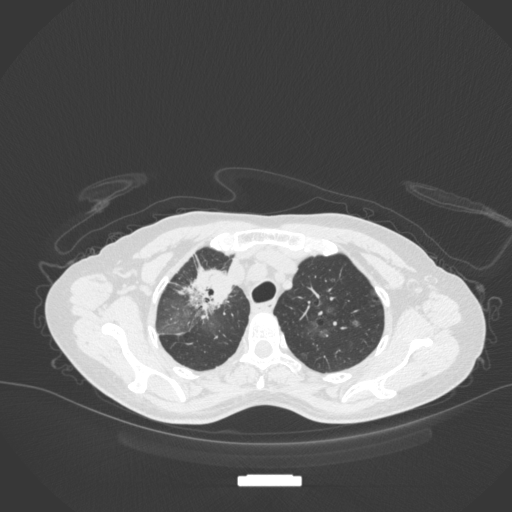
Chest CT, one axial slice. Position 261 of 311 along the scan axis. Lung window (W 1500 / L -600 HU). 1 mm slice thickness. 512 × 512 image matrix, field of view 400 × 400 mm. Female patient, age 59 years. Case-level facts recorded for this patient, not image findings: clinical TNM (as recorded): T3 N0 M0.
Outlined on this slice (bounding box drawn by a radiologist):
- lung tumour (recorded histology: adenocarcinoma): bounding box (x1, y1, x2, y2) in pixels: (180, 264, 233, 321)